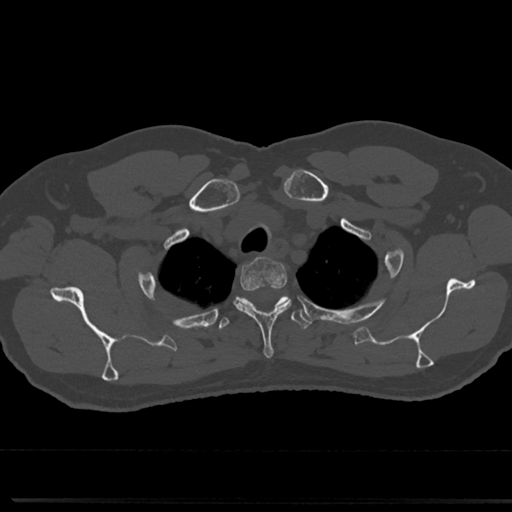
CT including the spine, one axial slice. Position 620 of 817 along the scan axis. Reconstruction kernel Br40s/3. 120 kVp. Bone window (W 1800 / L 400 HU). 0.5 mm slice thickness. 512 × 512 image matrix. Patient: male, 61 years. Case-level facts recorded for this patient, not image findings: primary cancer: prostate.
Annotated regions visible in this slice (semi-automatic segmentation, software-assisted and operator-edited):
- T2 vertebra: box from (x=235, y=260) to (x=288, y=353) px
- T3 vertebra: (x=215, y=294)–(x=314, y=333)